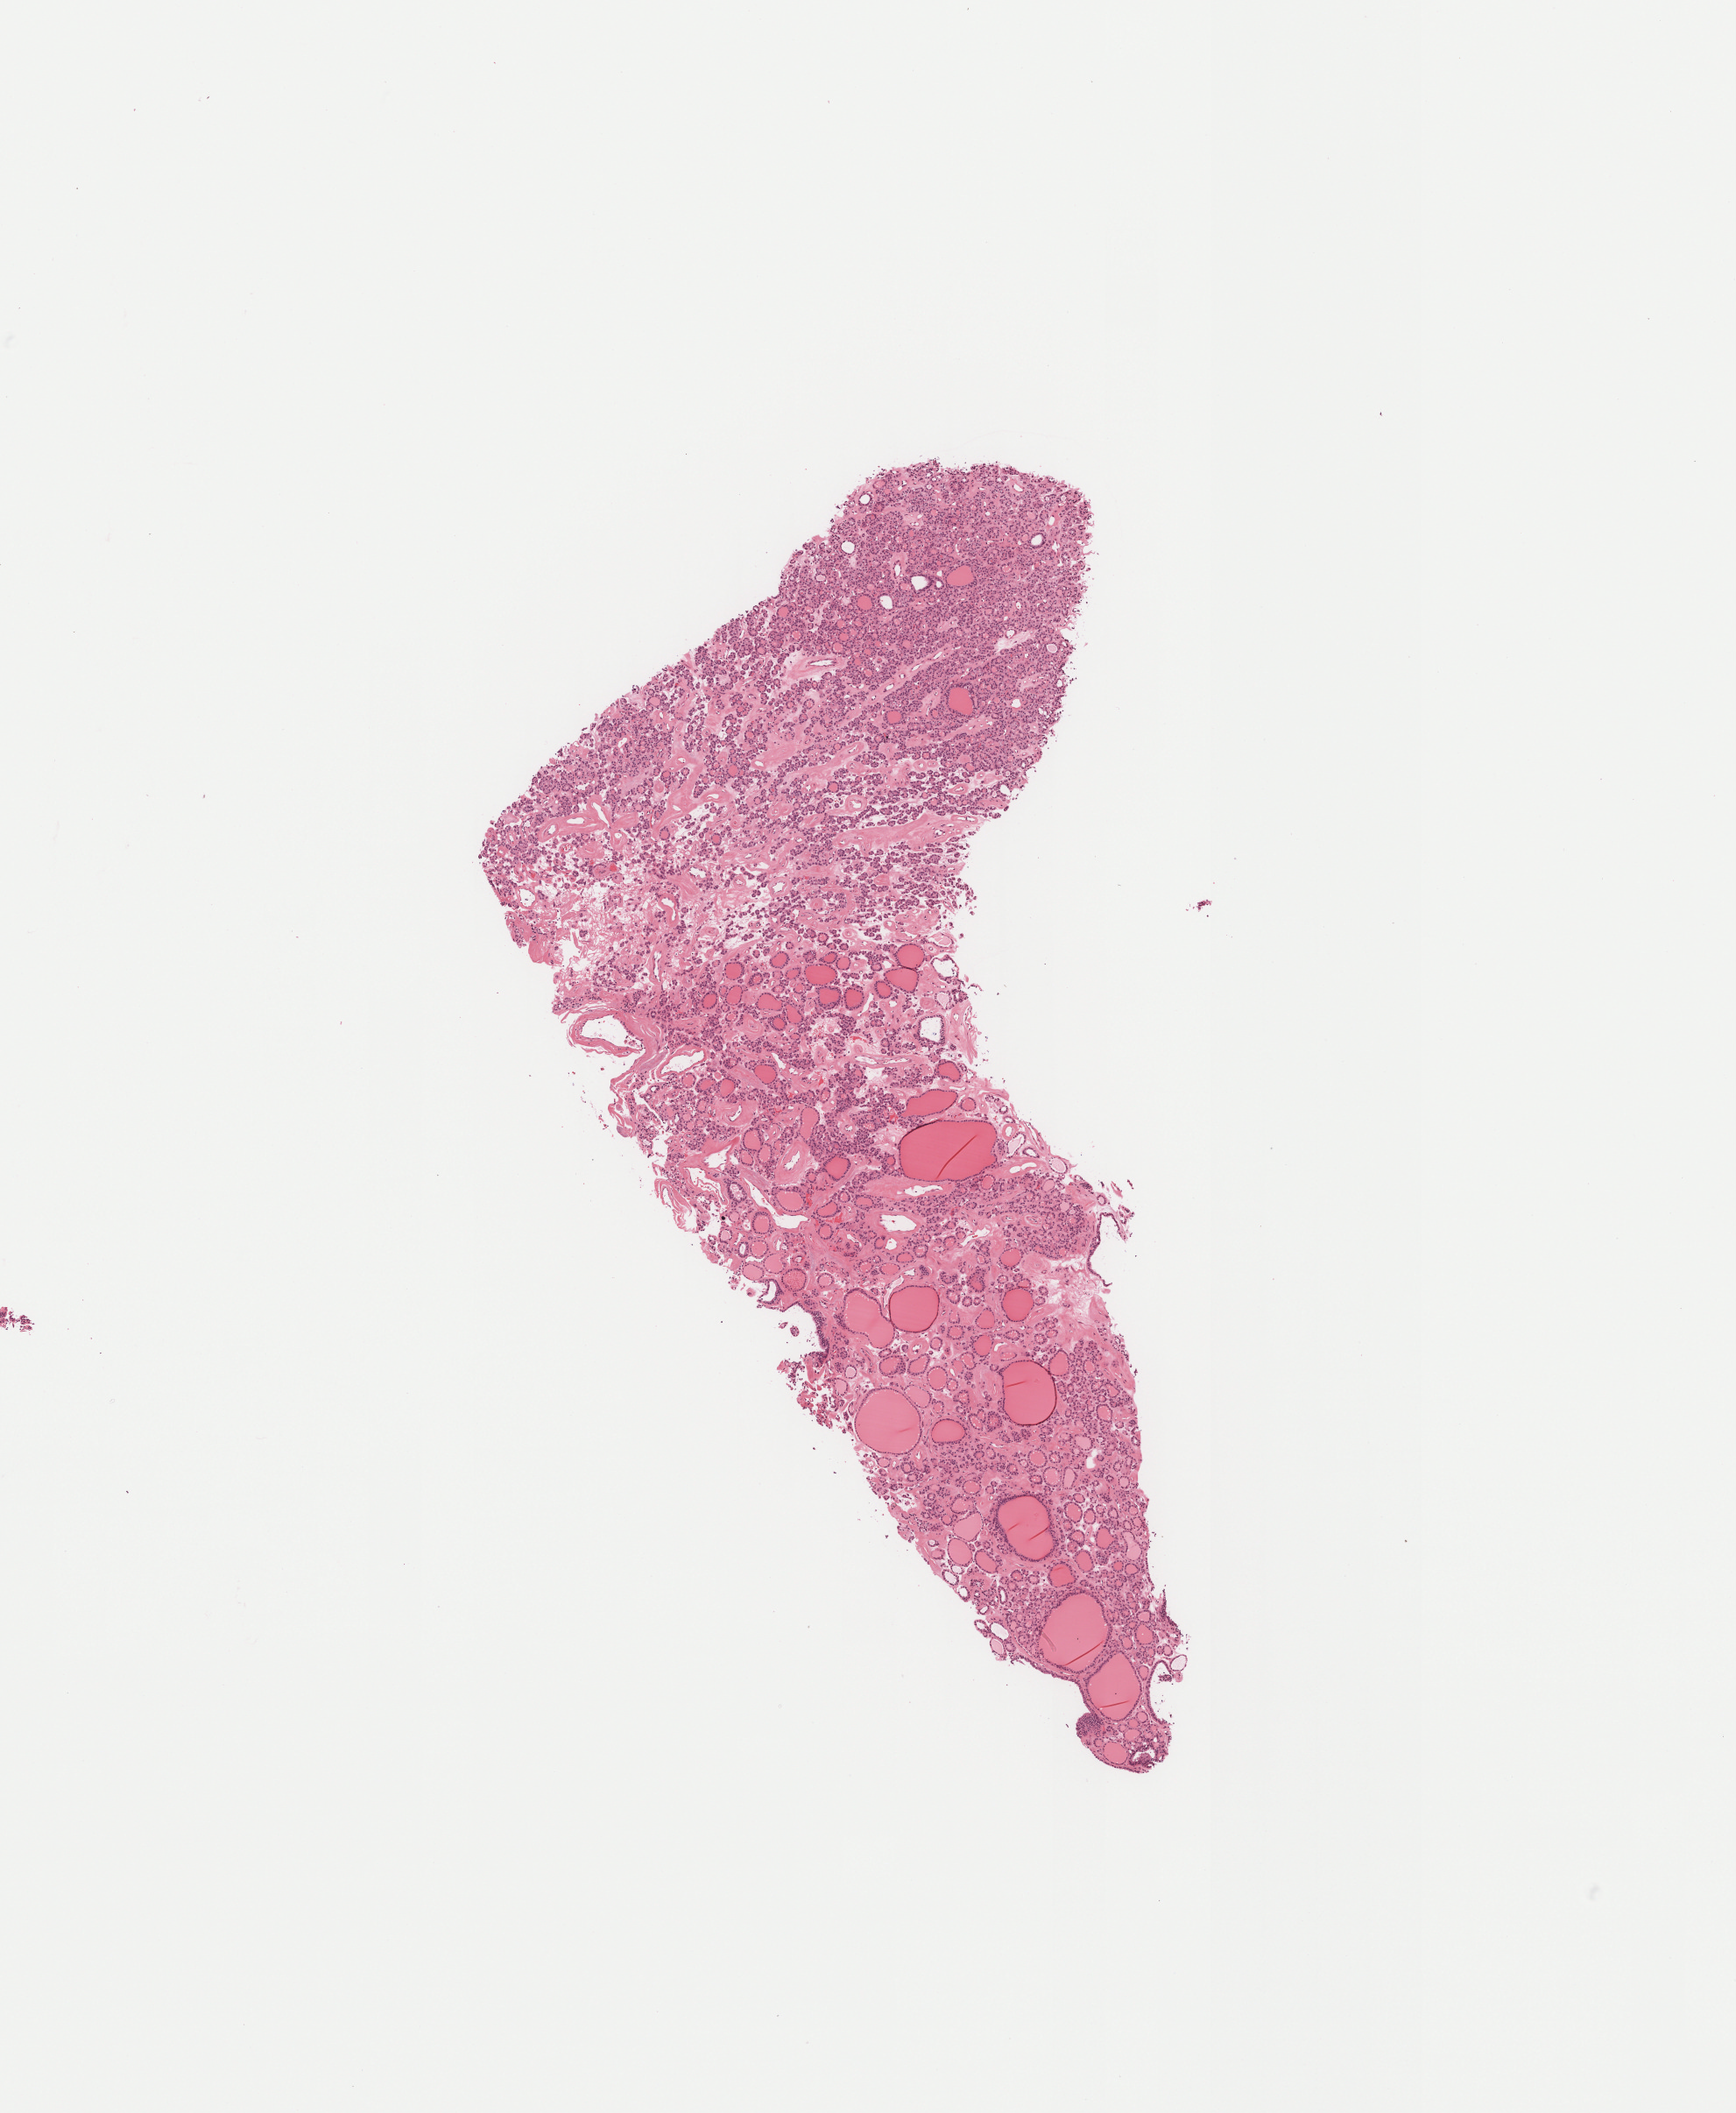
Digitized H&E-stained tissue section (whole slide), whole scanned area (about 8.0 x 9.7 mm) shown as a low-resolution overview; formalin-fixed paraffin-embedded (FFPE) diagnostic section; sample: primary tumour, thyroid. Female, age 49 years at initial diagnosis.
* laterality: left
* pathologic diagnosis: Papillary carcinoma, follicular variant (thyroid gland)
* AJCC pathologic stage: I